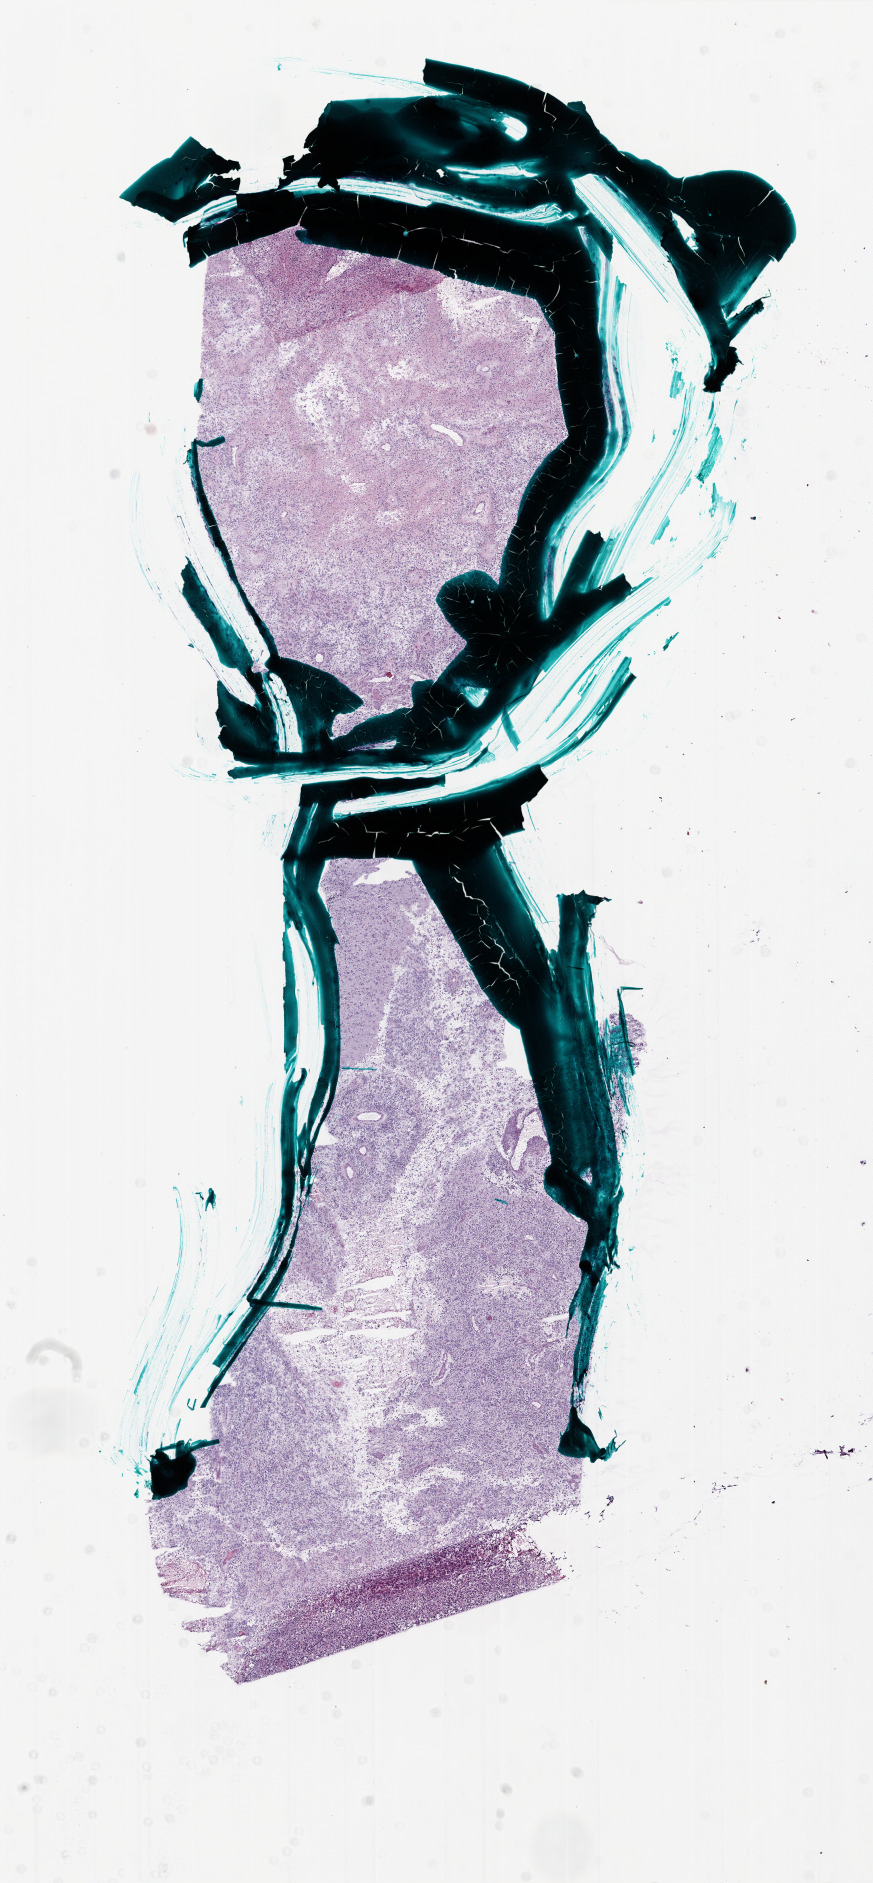
H&E-stained whole-slide image — shown as a low-resolution overview of the whole scanned area (about 7.0 x 15.1 mm, slide scanned at 20x), frozen section, primary tumour sample from the brain. Female, age 65 years at initial diagnosis. Pathologist review of this section (percent, as recorded): tumour cells 90%, tumour nuclei 100%.
Pathologic diagnosis: Glioblastoma.